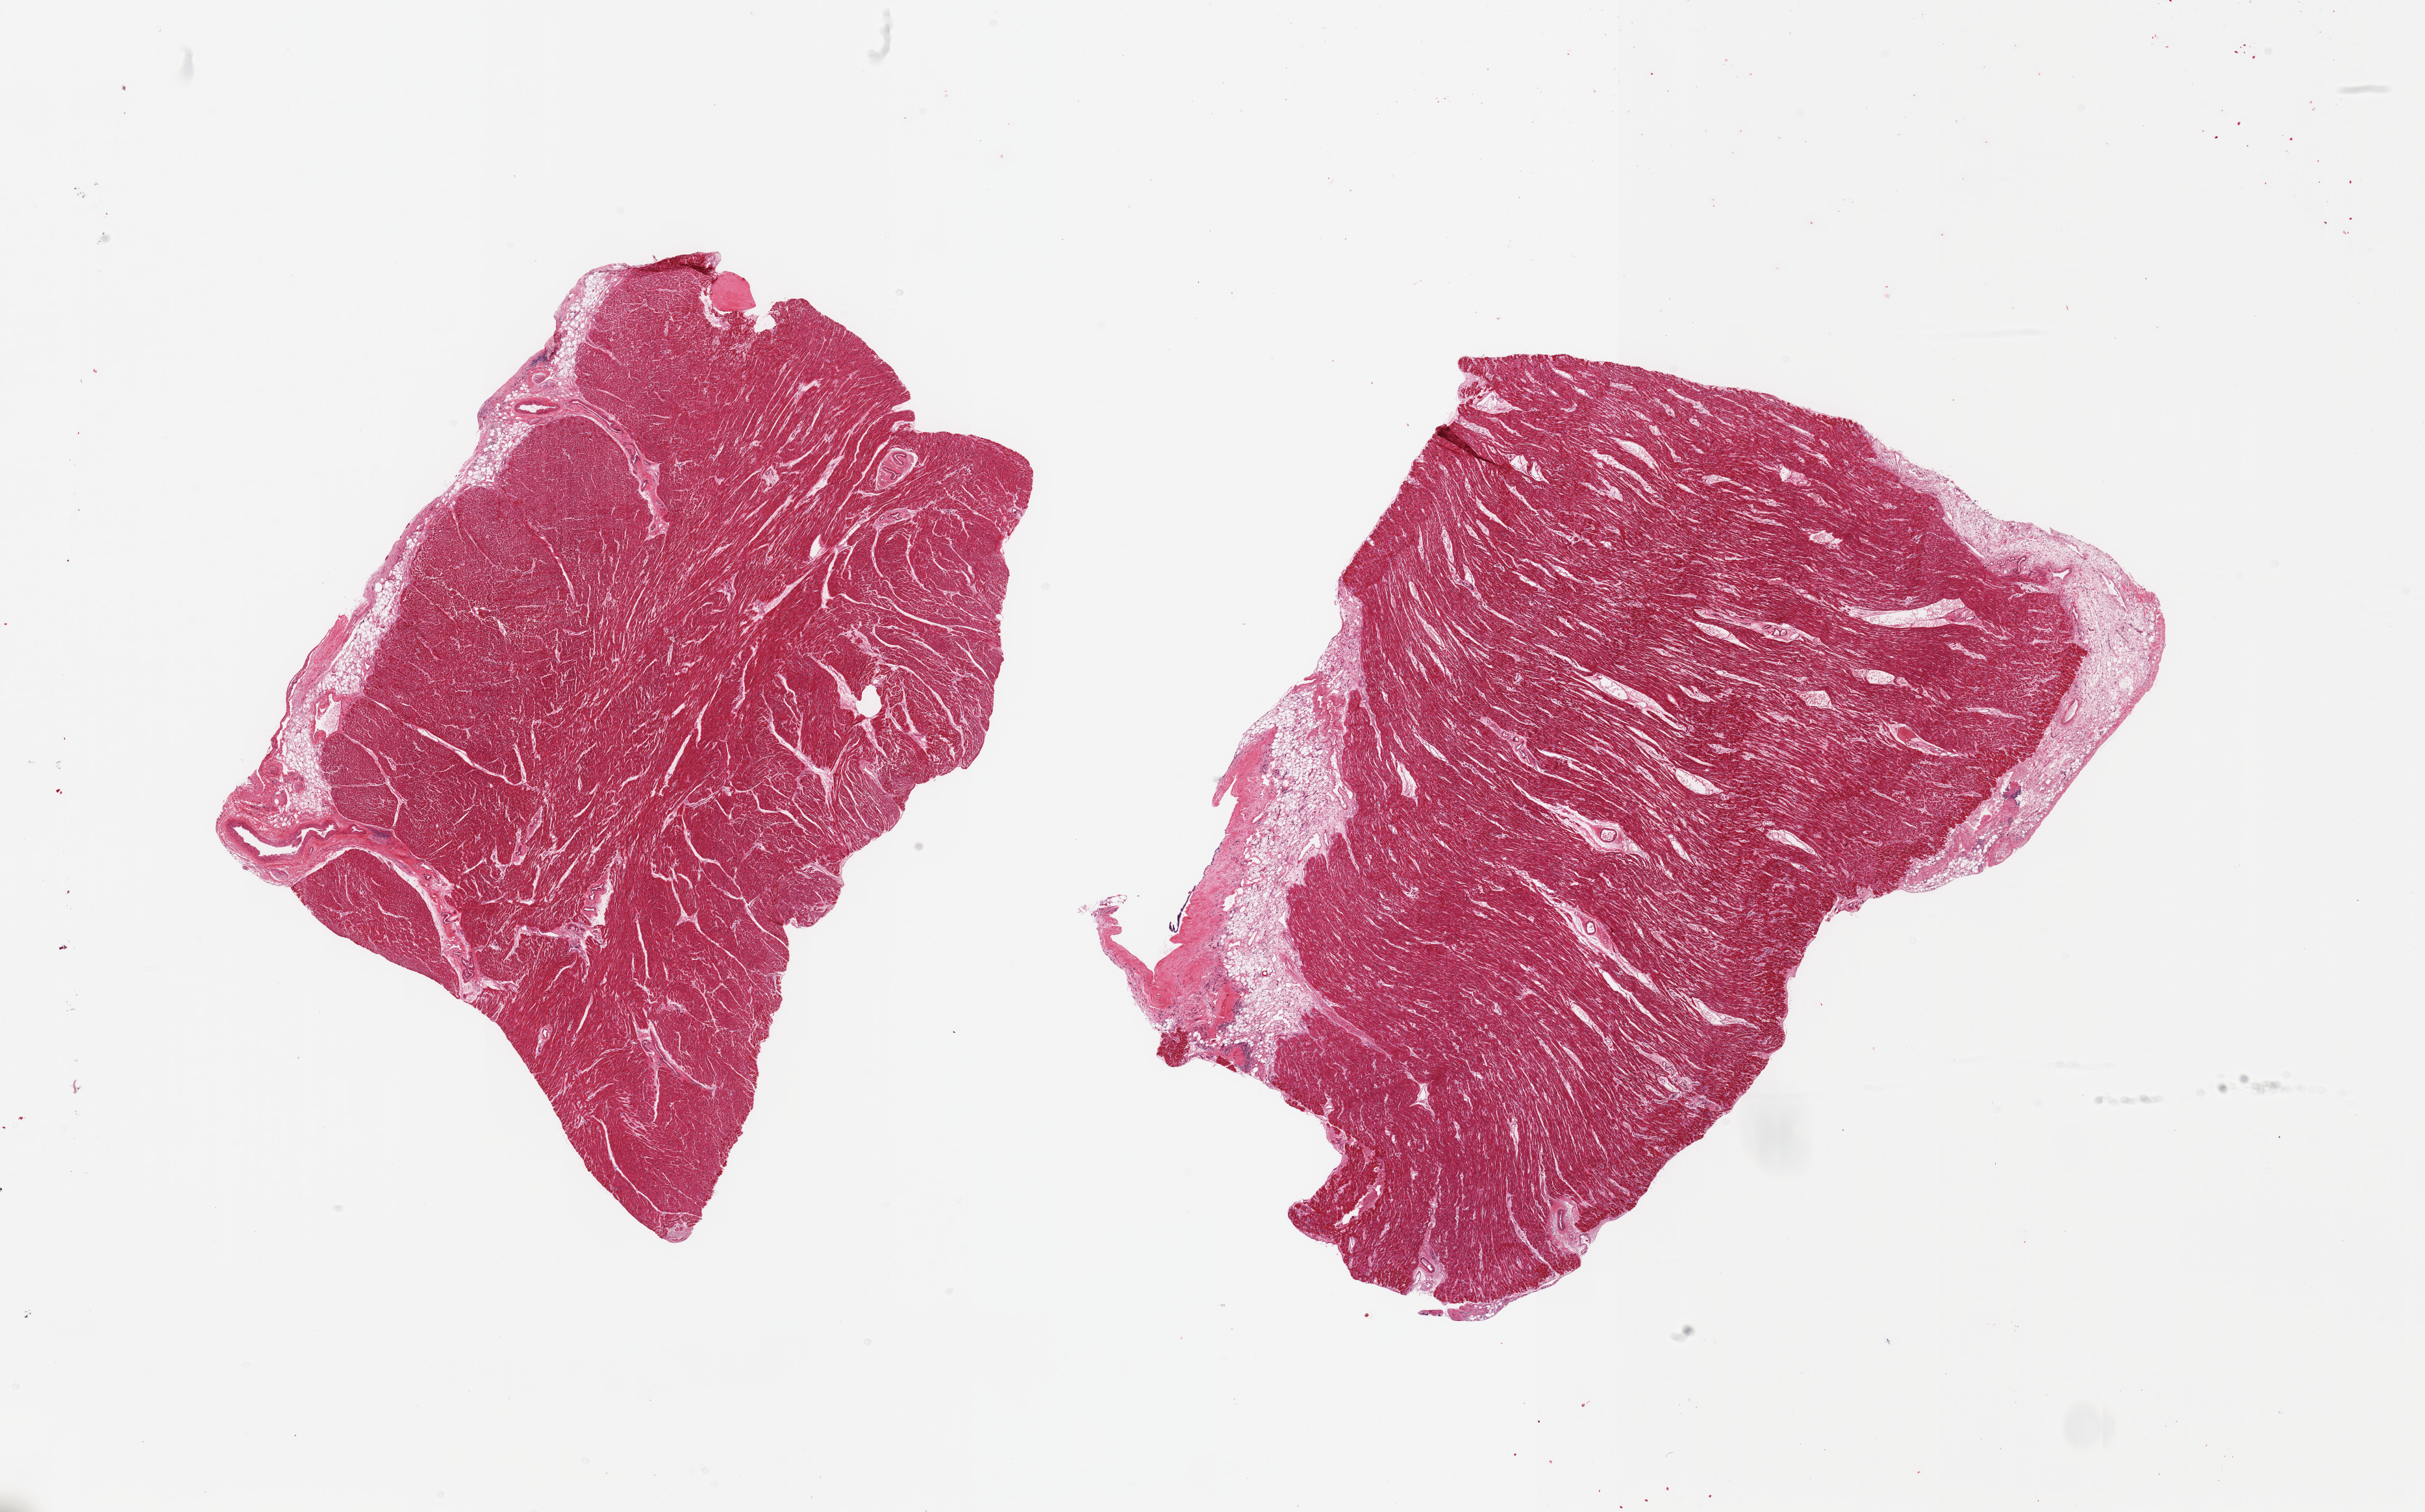
Whole-slide image, hematoxylin and eosin (H&E) stain, whole scanned area (about 29.5 x 18.4 mm, from a 20x scan) shown as a low-resolution overview; PAXgene-fixed paraffin-embedded (PFPE) section; sampled site (target tissue): heart; tissue donor sample. Donor sex: male.
Reviewer comment on this tissue sample: 2 pieces; small attachment of fat.